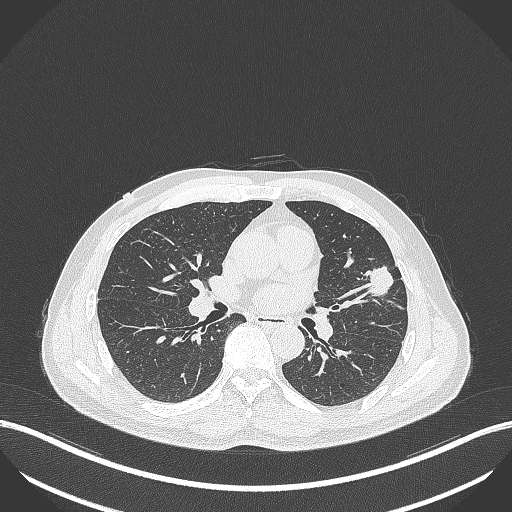
Chest CT, one axial slice. Slice 212 of 418 in the series (ordered by position). Reconstruction kernel B70f. 120 kVp. Lung window (W 1500 / L -600 HU). 512 × 512 image matrix. Patient: male, 55 years. Case-level facts recorded for this patient, not image findings: clinical TNM (as recorded): T1c N0 M0.
Annotated regions visible in this slice (rectangle marked by the reading radiologist):
- lung tumour (recorded histology: adenocarcinoma): bounding box (x1, y1, x2, y2) in pixels: (362, 260, 396, 300)